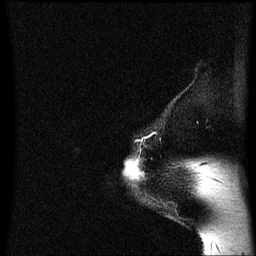
Breast MRI (dynamic contrast-enhanced), one sagittal slice; position 56 of 60 along the scan axis; dynamic contrast-enhanced series, image 2 of 3 at this slice position (ordered by acquisition); 1.5 T; TE 4.2 ms, TR 8.4 ms; 256 × 256 image matrix, field of view 200 × 200 mm. Female patient, age 54 years. Case-level facts recorded for this patient, not image findings: setting: breast cancer imaged before/during neoadjuvant chemotherapy; receptor status: HR-positive, HER2-negative.
Structures marked on this image (semi-automatically segmented with operator editing):
- analysis volume of interest (the breast-tissue region the enhancement analysis was run in; not a lesion): bounding box [x1, y1, x2, y2] px = [129, 158, 144, 179]
- tumour enhancement mask (voxels above the 70 % enhancement threshold inside the analysis volume of interest): [129, 160, 143, 179]